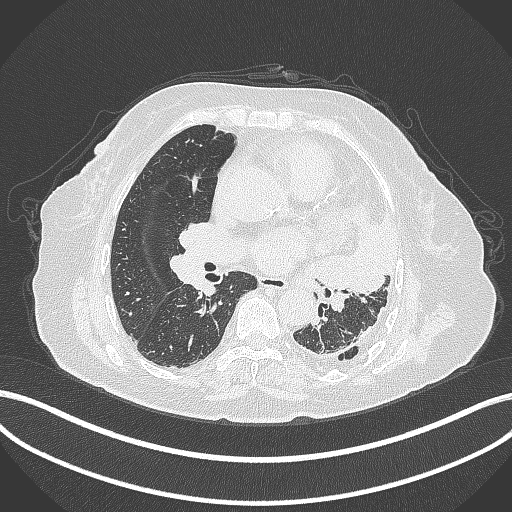
Chest CT, one axial slice; slice 189 of 399 in the series (ordered by position); lung window (W 1500 / L -600 HU); 1 mm slice thickness; 512 × 512 image matrix, field of view 400 × 400 mm. Patient: female, 75 years. Case-level facts recorded for this patient, not image findings: clinical TNM (as recorded): T3 N3 M1.
Annotated regions visible in this slice (bounding box drawn by a radiologist):
- lung tumour (recorded histology: adenocarcinoma): box from (x=315, y=206) to (x=402, y=298) px